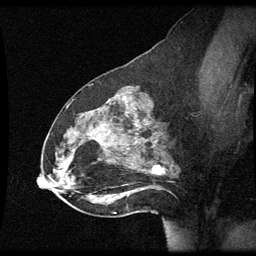
Breast MRI (dynamic contrast-enhanced), one sagittal slice; slice 33 of 60 in the series (ordered by position); dynamic contrast-enhanced series, image 2 of 3 at this slice position (ordered by acquisition); 1.5 T; TE 4.2 ms, TR 8.9 ms; 2 mm slice thickness; 256 × 256 image matrix, field of view 200 × 200 mm. Patient: female, 49 years. Case-level facts recorded for this patient, not image findings: setting: breast cancer imaged before/during neoadjuvant chemotherapy; receptor status: HR-positive, HER2-negative.
Annotated regions visible in this slice (semi-automatic segmentation, software-assisted and operator-edited):
- analysis volume of interest (the breast-tissue region the enhancement analysis was run in; not a lesion): bounding box (x1, y1, x2, y2) in pixels: (46, 92, 177, 205)
- tumour enhancement mask (voxels above the 70 % enhancement threshold inside the analysis volume of interest): (153, 166, 157, 171)